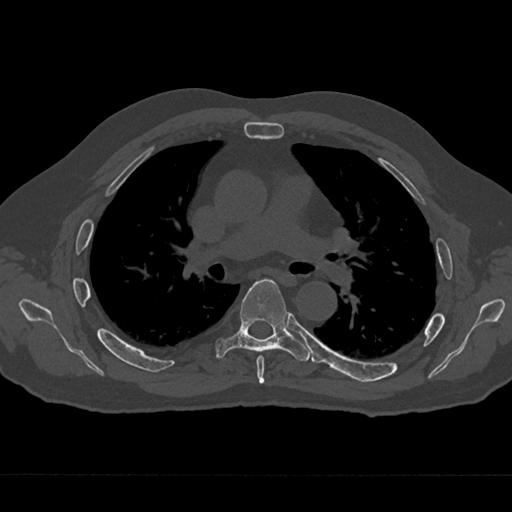
CT including the spine, one axial slice; slice 434 of 797 in the series (ordered by position); reconstruction kernel Br40s/3; bone window (W 1800 / L 400 HU); 512 × 512 image matrix, field of view 377 × 377 mm. Patient: male, 75 years. From the clinical record (not read from this slice): primary cancer: renal; vertebrae with lytic lesions (as recorded): T4.
Annotated regions visible in this slice (semi-automatically segmented with operator editing):
- T5 vertebra: box from (x=256, y=355) to (x=265, y=384) px
- T6 vertebra: (x=215, y=279)–(x=310, y=362)